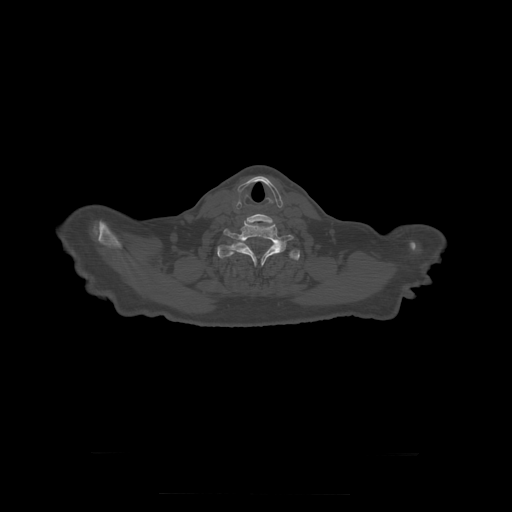
CT including the spine, one axial slice. Position 296 of 397 along the scan axis. Reconstruction kernel STANDARD. Bone window (W 1800 / L 400 HU). 1.25 mm slice thickness. 512 × 512 image matrix, field of view 510 × 510 mm. Patient age 73 years. From the clinical record (not read from this slice): primary cancer: prostate.
Annotated regions visible in this slice (semi-automatically segmented with operator editing):
- T1 vertebra: box from (x=217, y=239) to (x=300, y=265) px